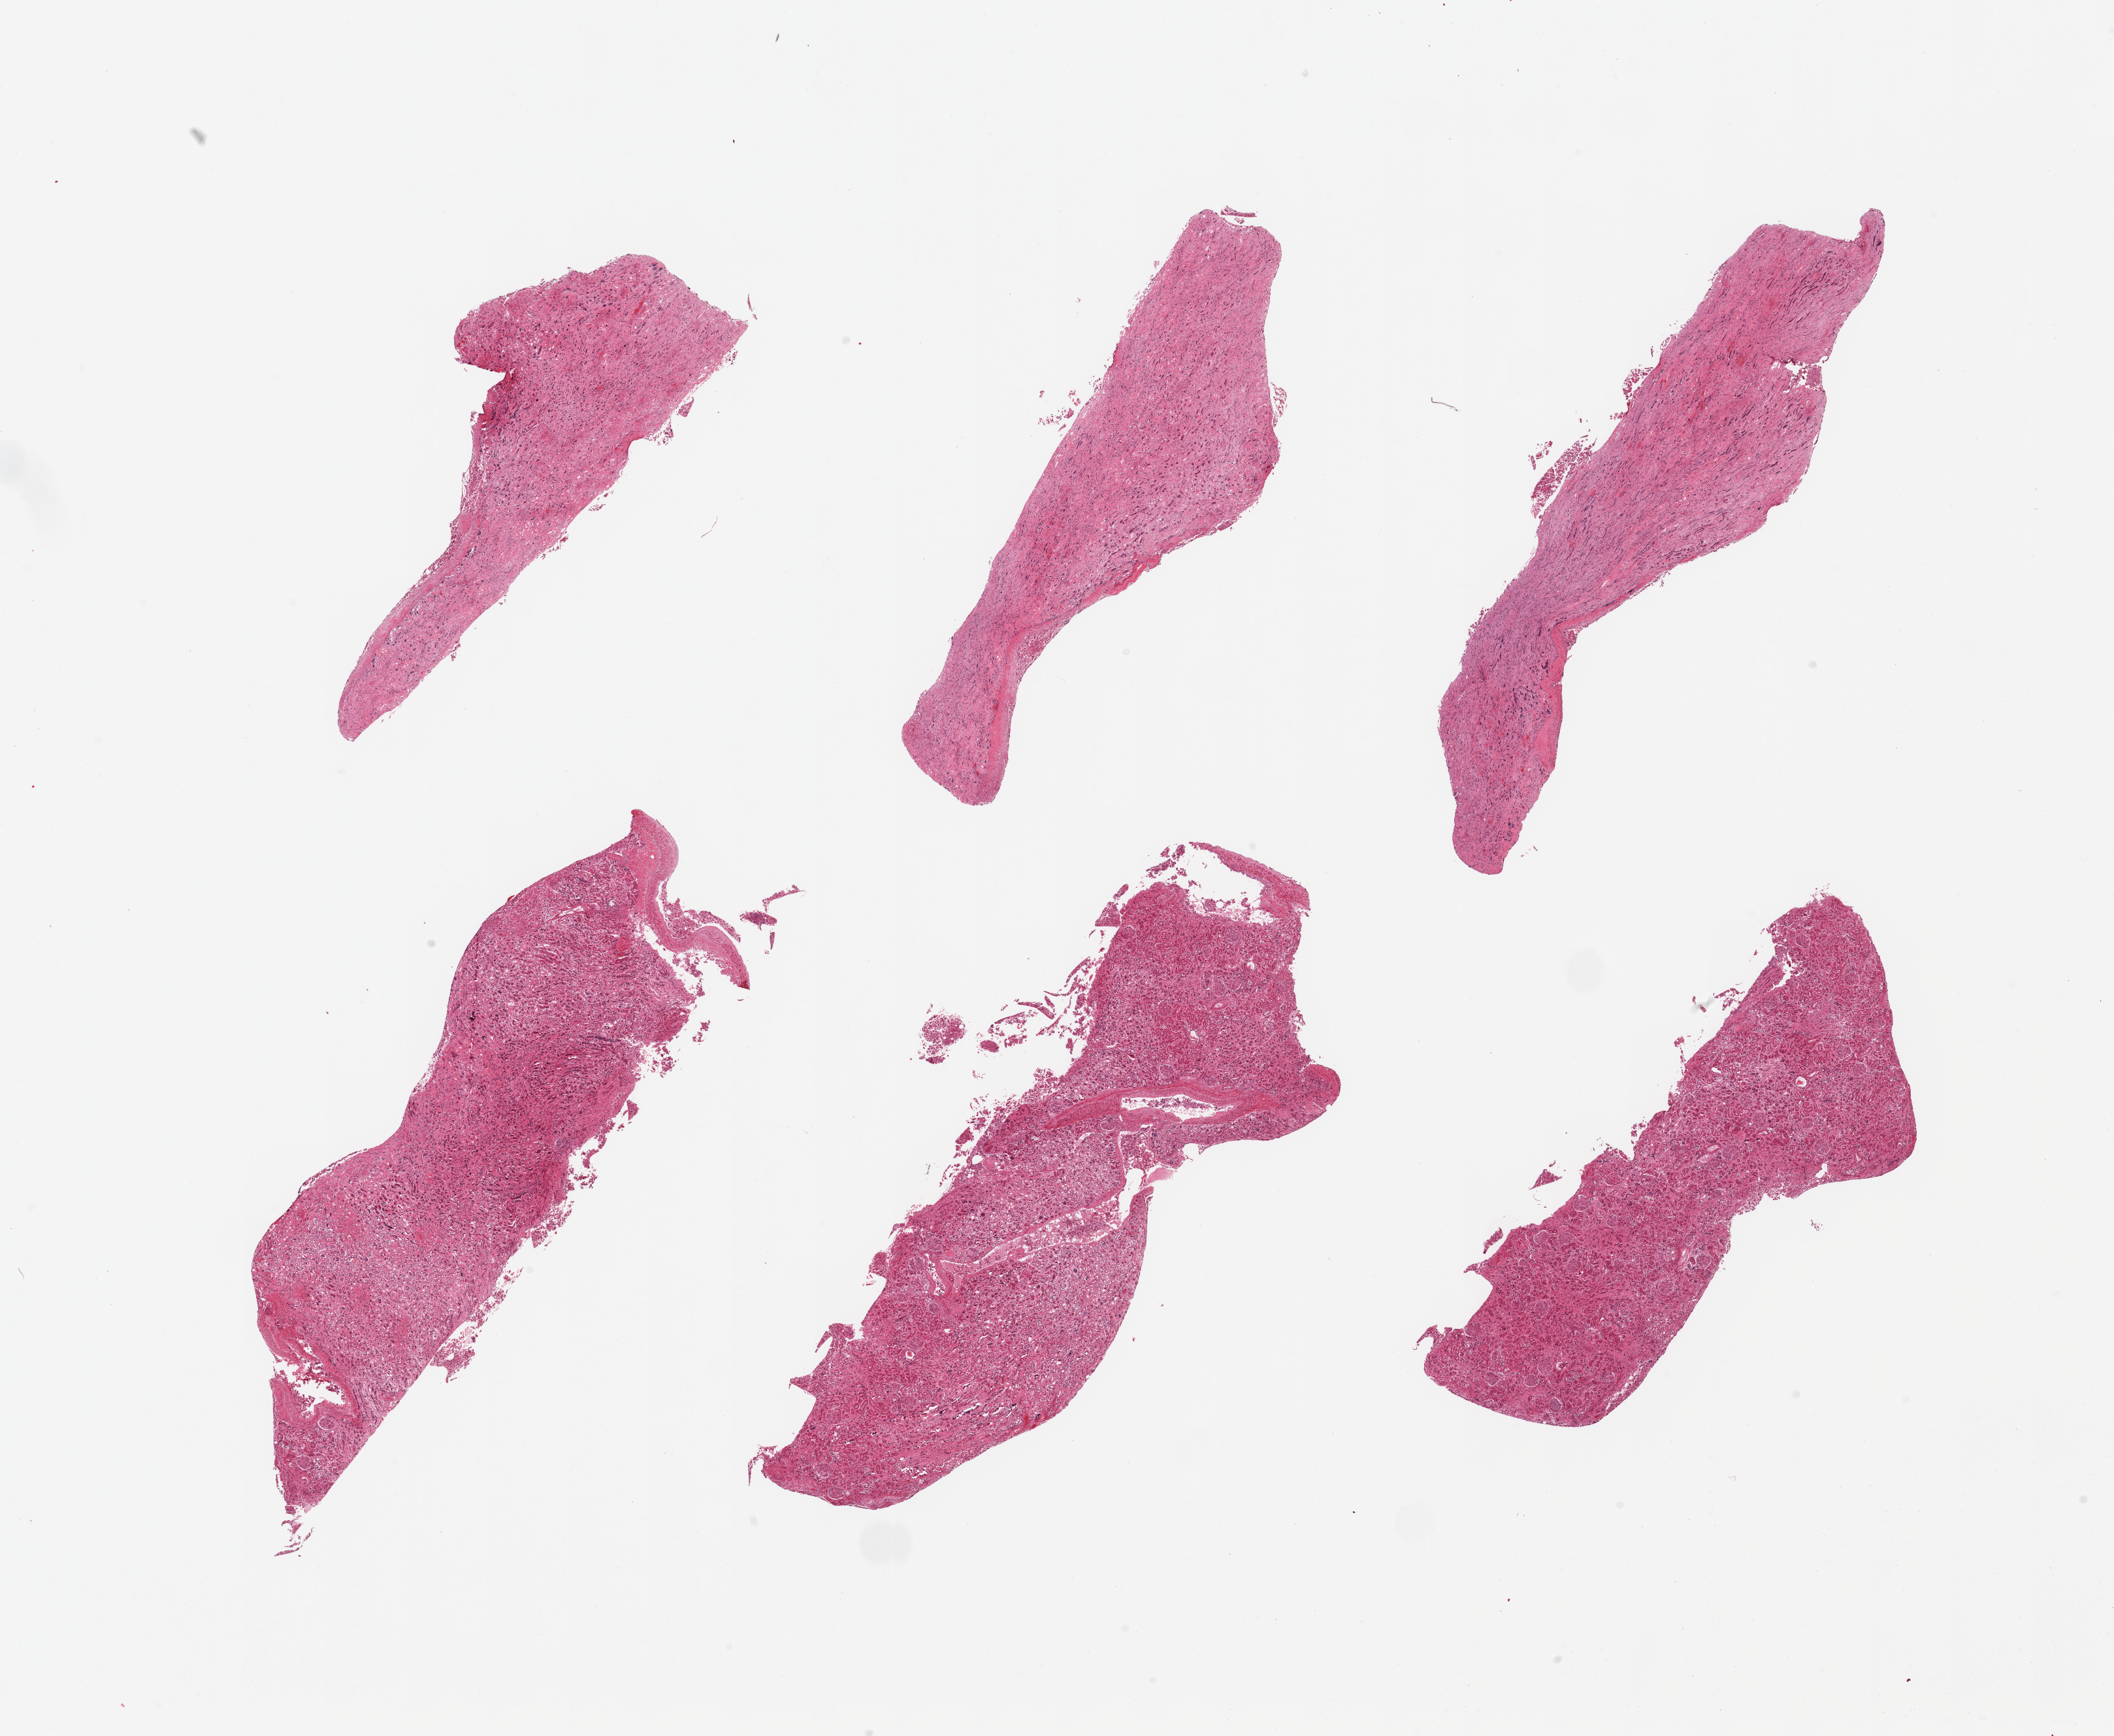
Digitized H&E-stained section — whole scanned area (about 25.6 x 21.0 mm) shown as a low-resolution overview, PAXgene-fixed paraffin-embedded (PFPE) section, sampled site (target tissue): renal cortex, tissue donor sample. Male donor.
Reviewer comment on this tissue sample: 6 pieces; 4 pieces are medulla, 2 are cortex; no active or chronic lesions.